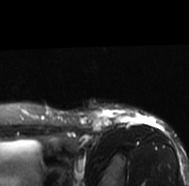
MRI of an extremity soft-tissue mass, one axial slice. Position 60 of 77 along the scan axis. T2-weighted fat-saturated. MR volume resampled by the dataset authors to the PET/CT grid (not the native acquisition matrix). 3.27 mm slice thickness. 189 × 186 image matrix. Female patient. From the clinical record (not read from this slice): histological type: leiomyosarcoma; grade: high; site of the primary tumour: groin.
Annotated regions visible in this slice (expert contour drawn on MRI and transferred to this co-registered scan by the dataset authors):
- gross tumour volume including surrounding oedema: bounding box [x1, y1, x2, y2] px = [88, 104, 157, 131]
- gross tumour volume (mass): [90, 118, 112, 130]